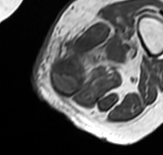
MRI of an extremity soft-tissue mass, one axial slice. Position 16 of 65 along the scan axis. MR volume resampled by the dataset authors to the PET/CT grid (not the native acquisition matrix). 163 × 155 image matrix. Female patient. From the clinical record (not read from this slice): histological type: pleomorphic leiomyosarcoma; grade: high; site of the primary tumour: left thigh.
Structures marked on this image (expert contour drawn on MRI and transferred to this co-registered scan by the dataset authors):
- gross tumour volume including surrounding oedema: bounding box [x1, y1, x2, y2] px = [51, 26, 136, 96]
- gross tumour volume (mass): [51, 58, 84, 96]